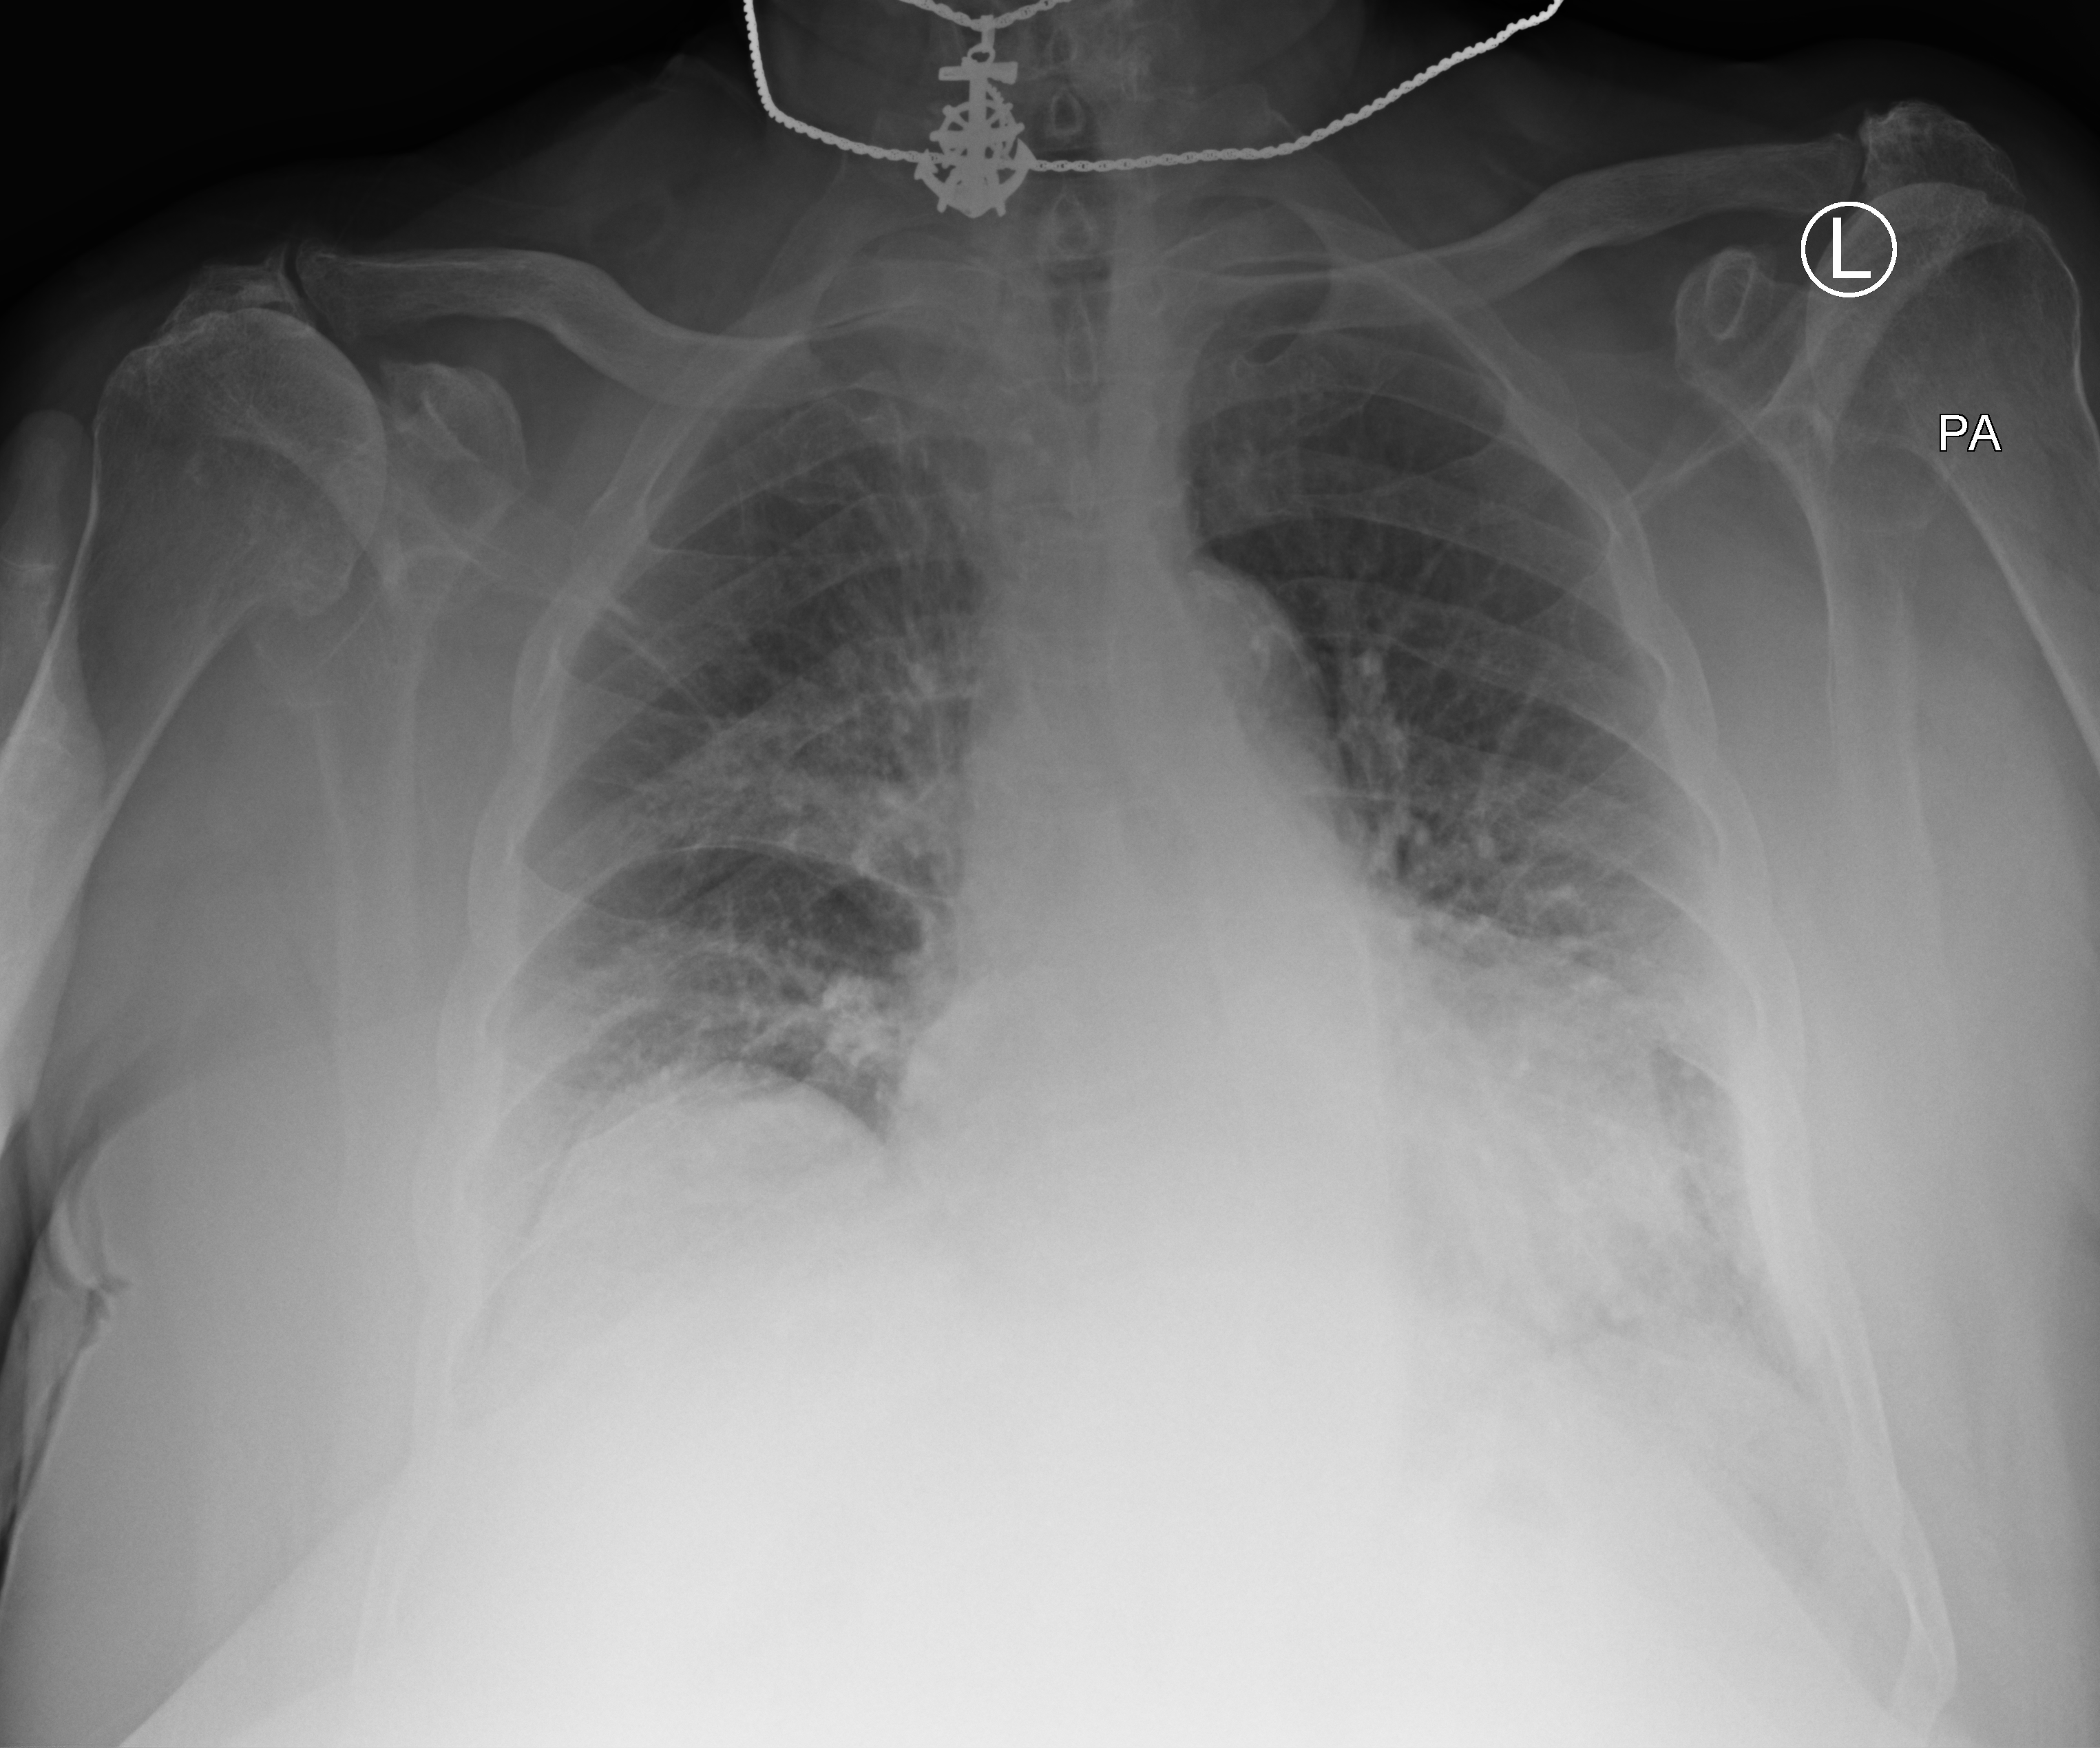
Chest X-ray (portable), anteroposterior (AP) projection. Patient hospitalised with COVID-19; male, aged 75–90 years.
Admission-level facts for this patient (not findings on this image; timing relative to this image not recorded): length of hospital stay: 6 days; admitted to intensive care during this hospital stay: no.